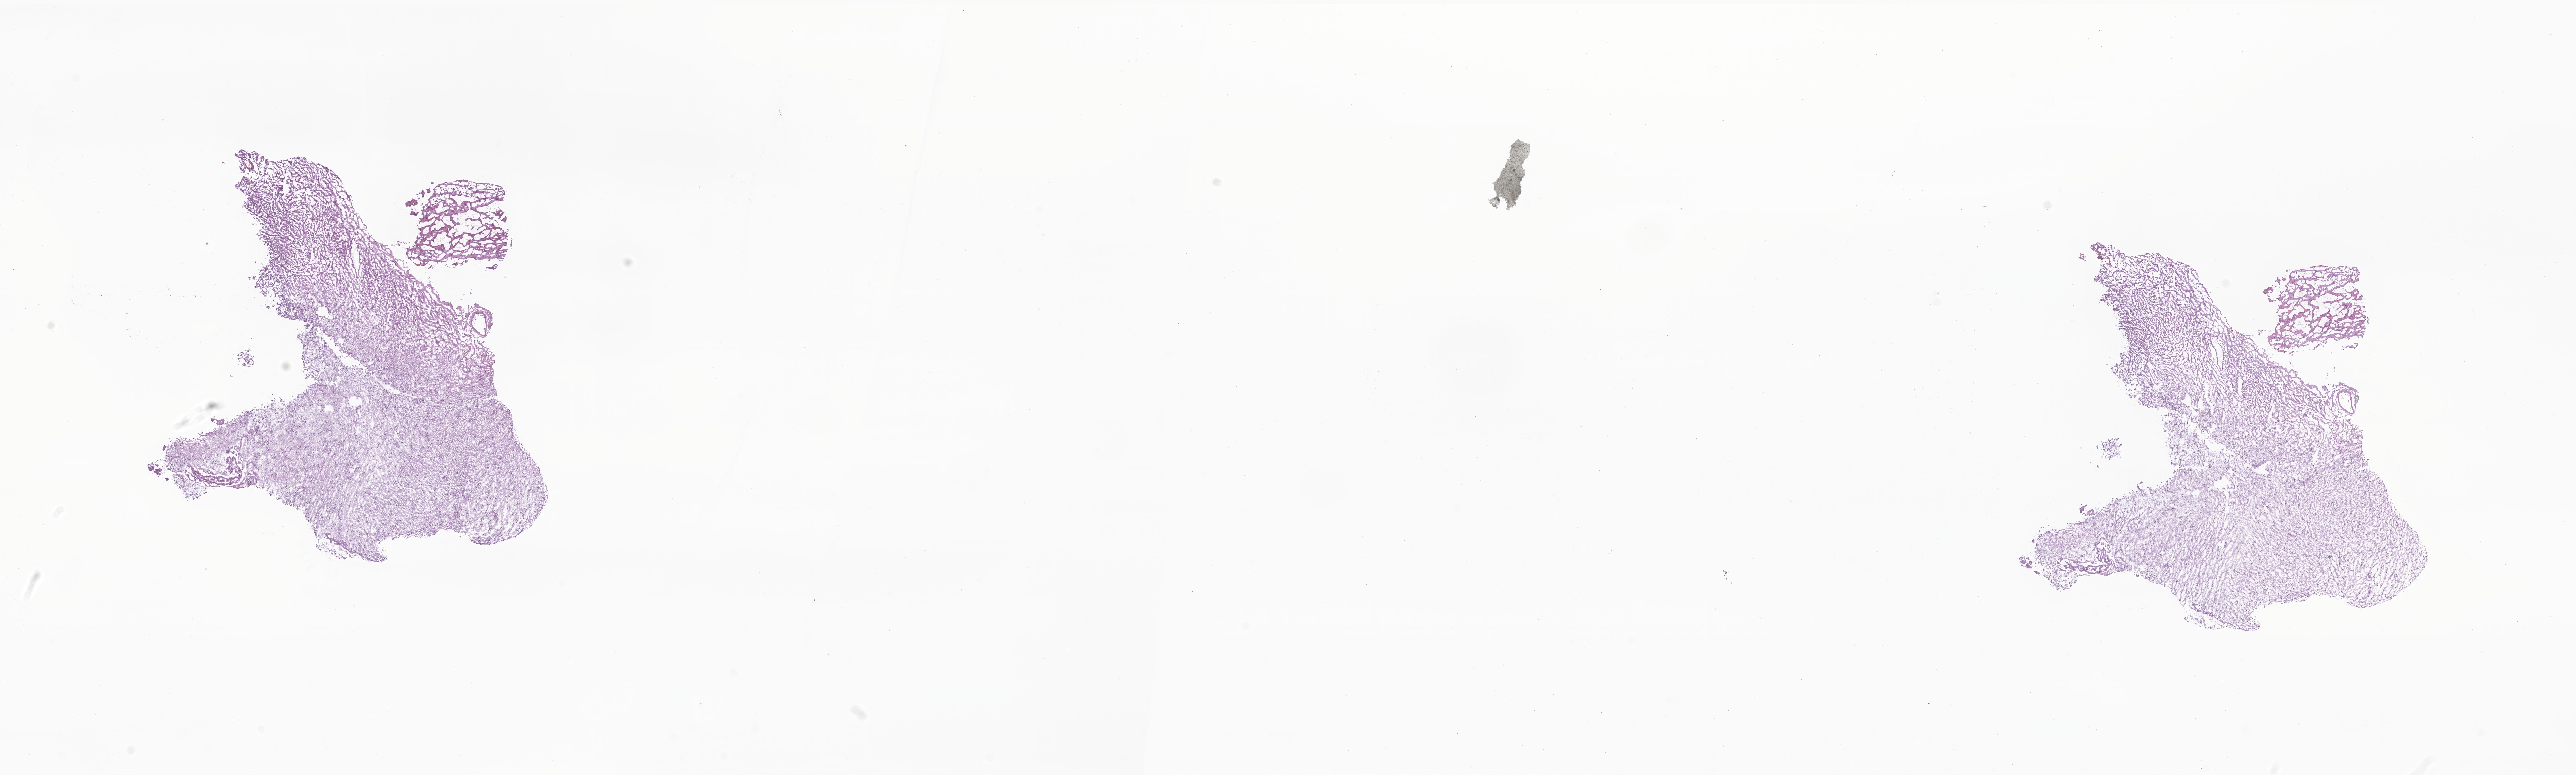
Digitized hematoxylin and eosin (H&E)-stained section of tumor tissue from the brain stem, a low-resolution overview of the entire scanned area, about 32.3 x 9.7 mm. Frozen section. Patient: male, age 53 months (4 years 5 months).
• diagnosis (ICD-O-3 morphology term): Pilocytic astrocytoma